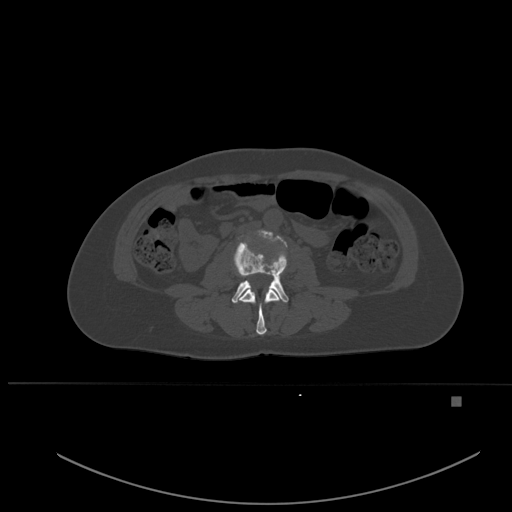
CT including the spine, one axial slice. Position 201 of 651 along the scan axis. Bone window (W 1800 / L 400 HU). 1.5 mm slice thickness. 512 × 512 image matrix, field of view 443 × 443 mm. Female patient, age 49 years. From the clinical record (not read from this slice): primary cancer: breast; vertebrae with lytic lesions (as recorded): L3, T12, L4.
Annotated regions visible in this slice (semi-automatic segmentation, software-assisted and operator-edited):
- L2 vertebra: box from (x=239, y=289) to (x=280, y=335) px
- L3 vertebra: (x=231, y=231)–(x=289, y=303)